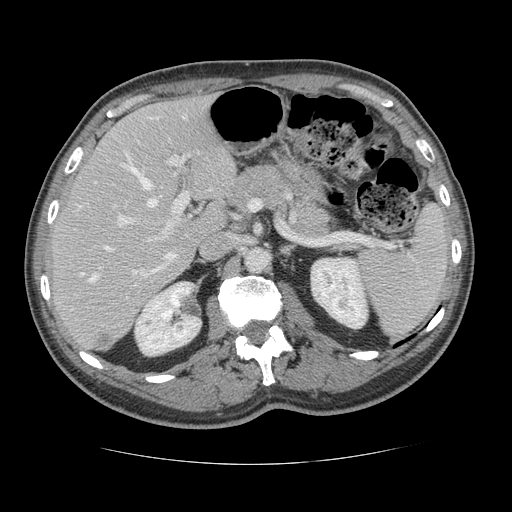
Contrast-enhanced abdominal CT, one axial slice; position 79 of 134 along the scan axis; soft-tissue window (W 400 / L 40 HU); 512 × 512 image matrix. Male patient, age 68 years. Case-level facts recorded for this patient, not image findings: diagnosis: colorectal cancer liver metastases, imaged before liver resection; multiple liver metastases: yes; largest metastasis: 2.2 cm; disease in both lobes: no.
Structures marked on this image (expert manual segmentation):
- hepatic veins: bounding box [x1, y1, x2, y2] px = [81, 117, 158, 282]
- liver: [50, 97, 236, 351]
- planned liver remnant (the part of the liver to remain after resection): [48, 97, 236, 339]
- portal vein (with intrahepatic branches): [114, 115, 191, 277]
- liver metastasis: [96, 334, 116, 350]